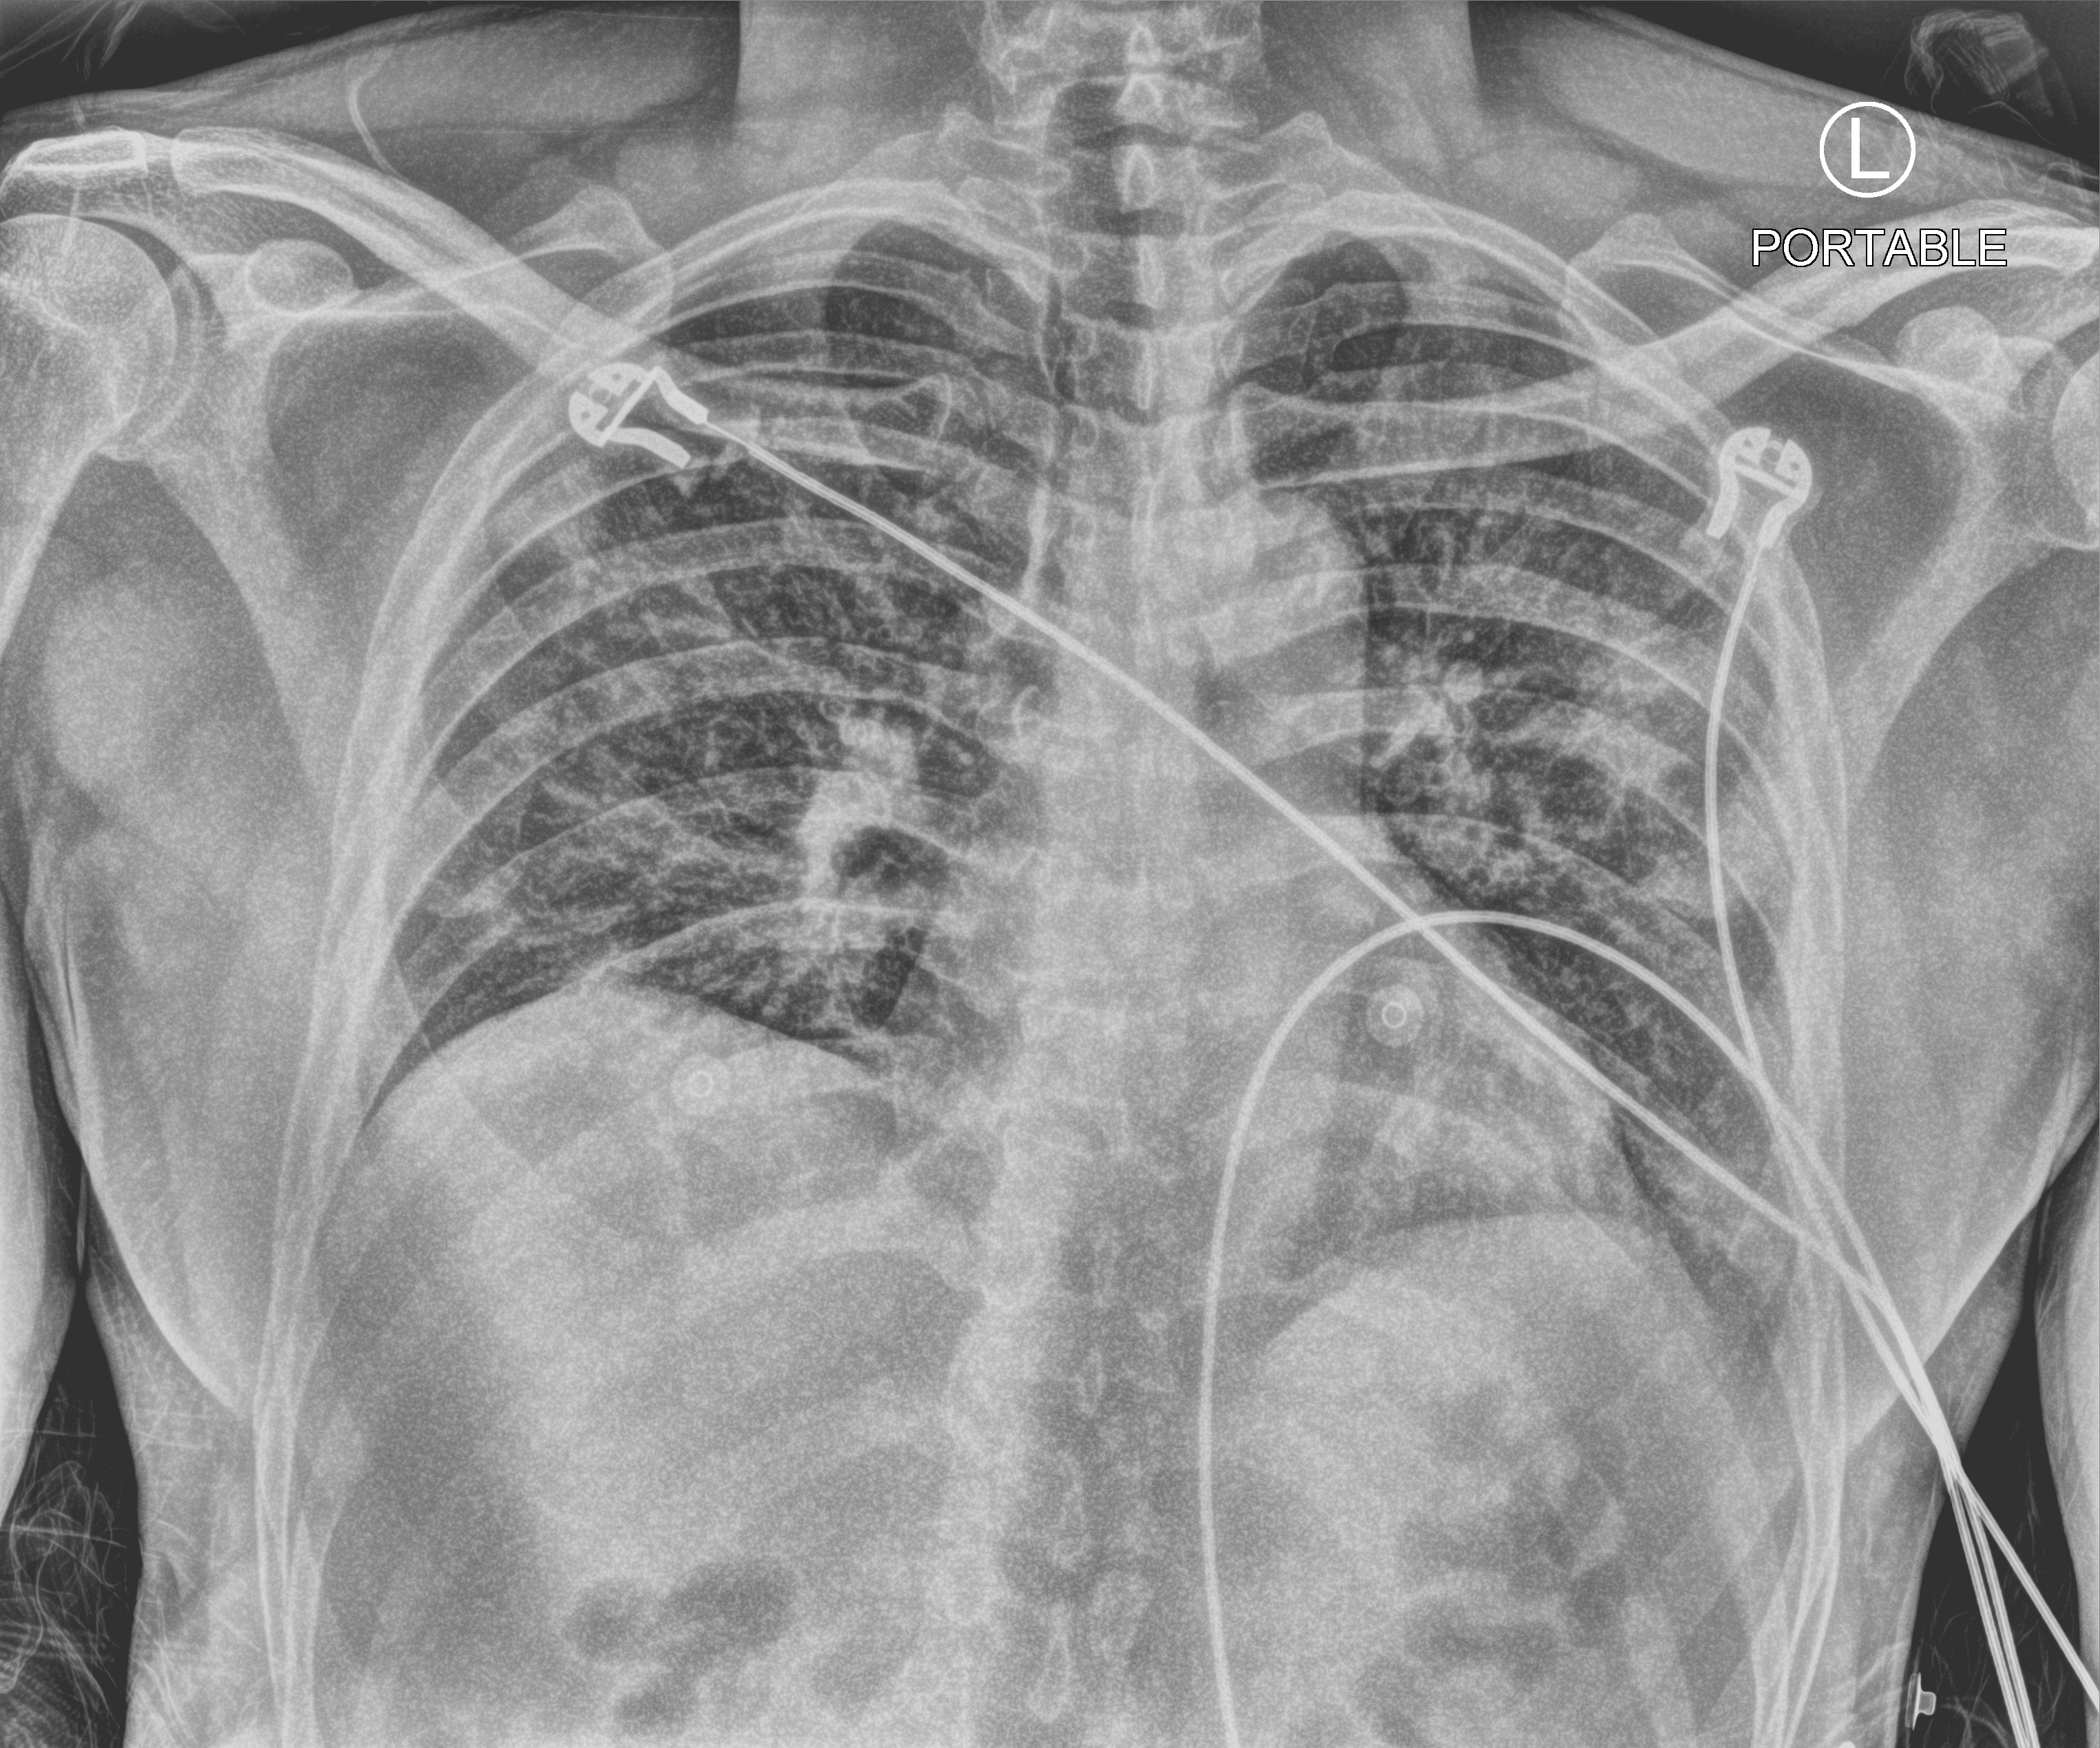
Portable chest radiograph. Patient hospitalised with COVID-19; male, aged 18–59 years.
Admission-level facts for this patient (not findings on this image; timing relative to this image not recorded): admitted to intensive care during this hospital stay: no; length of hospital stay: 2 days; mechanically ventilated during this hospital stay: no.